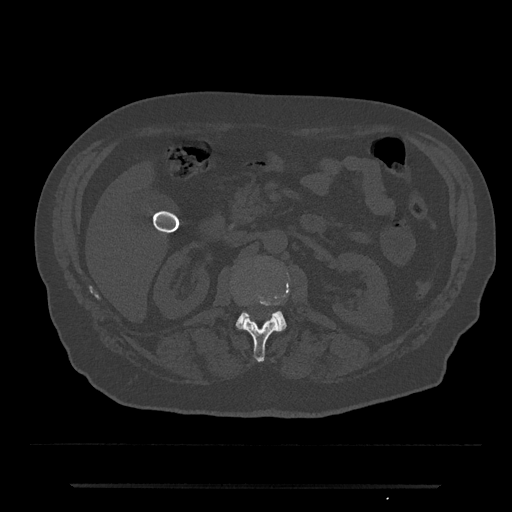
CT including the spine, one axial slice; position 509 of 797 along the scan axis; 120 kVp; bone window (W 1800 / L 400 HU); 0.5 mm slice thickness; 512 × 512 image matrix, field of view 434 × 434 mm. Patient: male, 80 years. From the clinical record (not read from this slice): primary cancer: prostate; vertebrae with lytic lesions (as recorded): L1, T11.
Annotated regions visible in this slice (semi-automatically segmented with operator editing):
- L1 vertebra: bounding box [x1, y1, x2, y2] px = [242, 301, 280, 362]
- L2 vertebra: [235, 297, 287, 332]